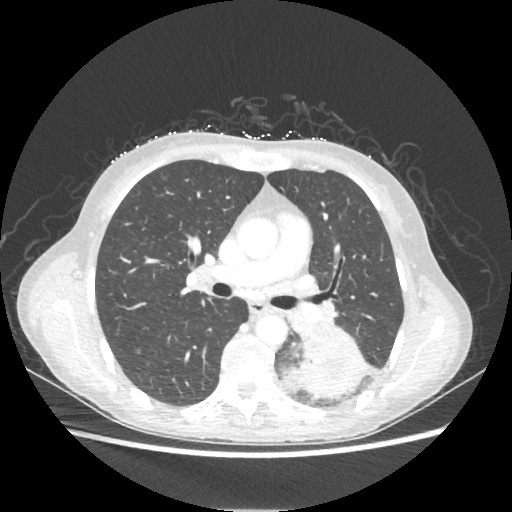
Chest CT, one axial slice. Slice 126 of 221 in the series (ordered by position). Reconstruction kernel STANDARD. 80 kVp. Lung window (W 1500 / L -600 HU). 1.25 mm slice thickness. 512 × 512 image matrix. Female patient, age 53 years. Case-level facts recorded for this patient, not image findings: clinical TNM (as recorded): T3 N0 M0.
Annotated regions visible in this slice (rectangle marked by the reading radiologist):
- lung tumour (recorded histology: adenocarcinoma): bounding box [x1, y1, x2, y2] px = [294, 327, 371, 398]